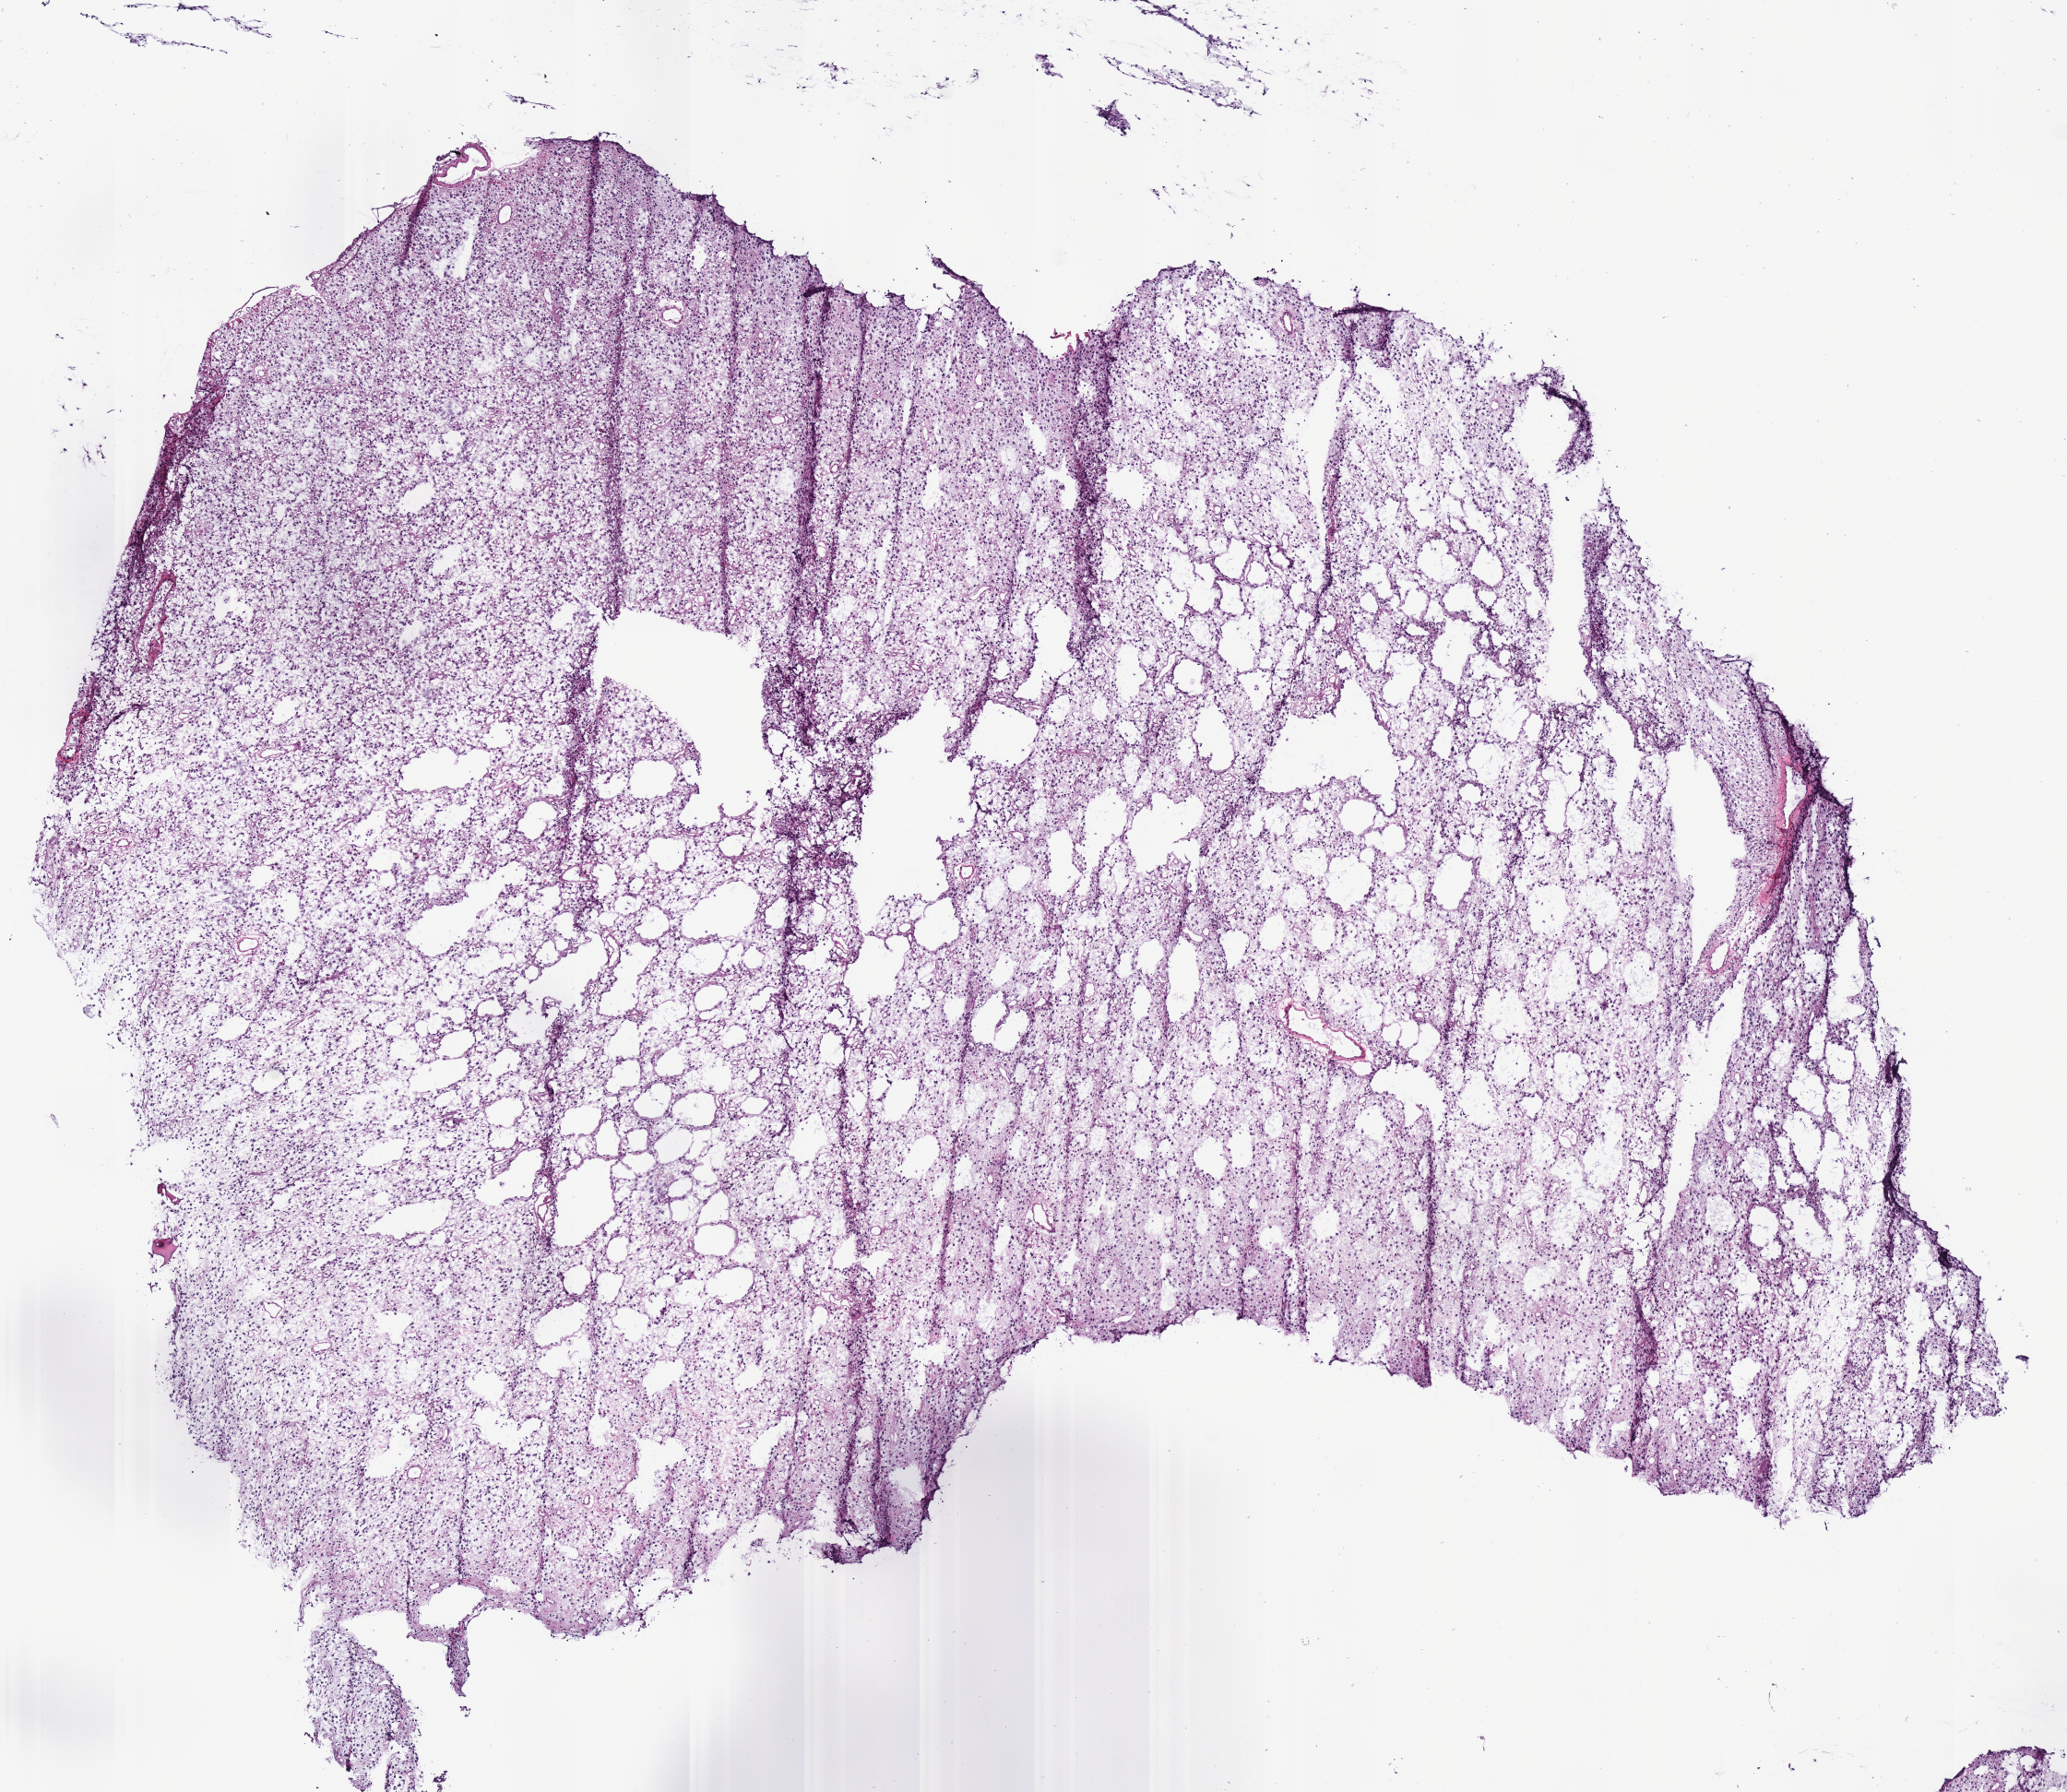
Whole-slide histology image, H&E — low-resolution overview of the scanned area, about 8.8 x 7.6 mm, frozen section from the bottom of the tissue portion, primary tumour sample from the brain. Patient: male, age at initial diagnosis 37 years. Composition of this section per pathologist review: tumour cells 100%, tumour nuclei 85%.
Diagnosis: Astrocytoma, anaplastic (cerebrum).